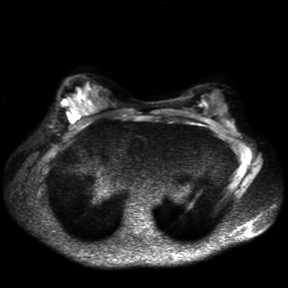
Breast MRI, one axial slice. Position 22 of 30 along the scan axis. Diffusion-weighted series; image 2 of 4 stored at this slice position (different b-values; order by instance number). 3 T. 288 × 288 image matrix, field of view 360 × 360 mm. Female patient.
Annotated regions visible in this slice (manually delineated by an expert):
- tumour on diffusion-weighted imaging: bounding box [x1, y1, x2, y2] px = [71, 114, 77, 119]